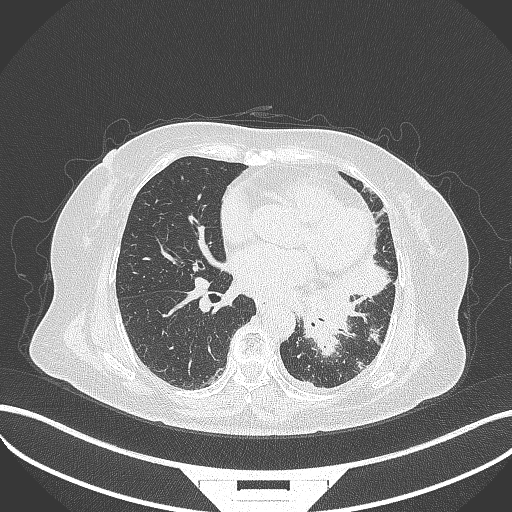
Chest CT, one axial slice; position 159 of 322 along the scan axis; reconstruction kernel B70f; 120 kVp; lung window (W 1500 / L -600 HU); 512 × 512 image matrix, field of view 400 × 400 mm. Female patient, age 69 years. From the clinical record (not read from this slice): clinical TNM (as recorded): T2b N3 M1.
Structures marked on this image (bounding box drawn by a radiologist):
- lung tumour (recorded histology: adenocarcinoma): box from (x=295, y=275) to (x=355, y=357) px